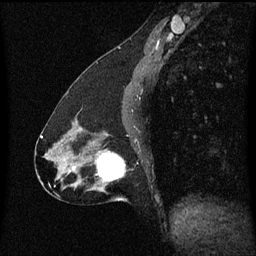
Breast MRI (dynamic contrast-enhanced), one sagittal slice. Position 28 of 60 along the scan axis. Dynamic contrast-enhanced series, image 2 of 3 at this slice position (ordered by acquisition). 1.5 T. TE 4.2 ms, TR 8.4 ms. 2 mm slice thickness. 256 × 256 image matrix. Female patient, age 47 years.
Outlined on this slice (semi-automatically segmented with operator editing):
- analysis volume of interest (the breast-tissue region the enhancement analysis was run in; not a lesion): bounding box [x1, y1, x2, y2] px = [81, 144, 125, 193]
- tumour enhancement mask (voxels above the 70 % enhancement threshold inside the analysis volume of interest): [97, 154, 125, 183]